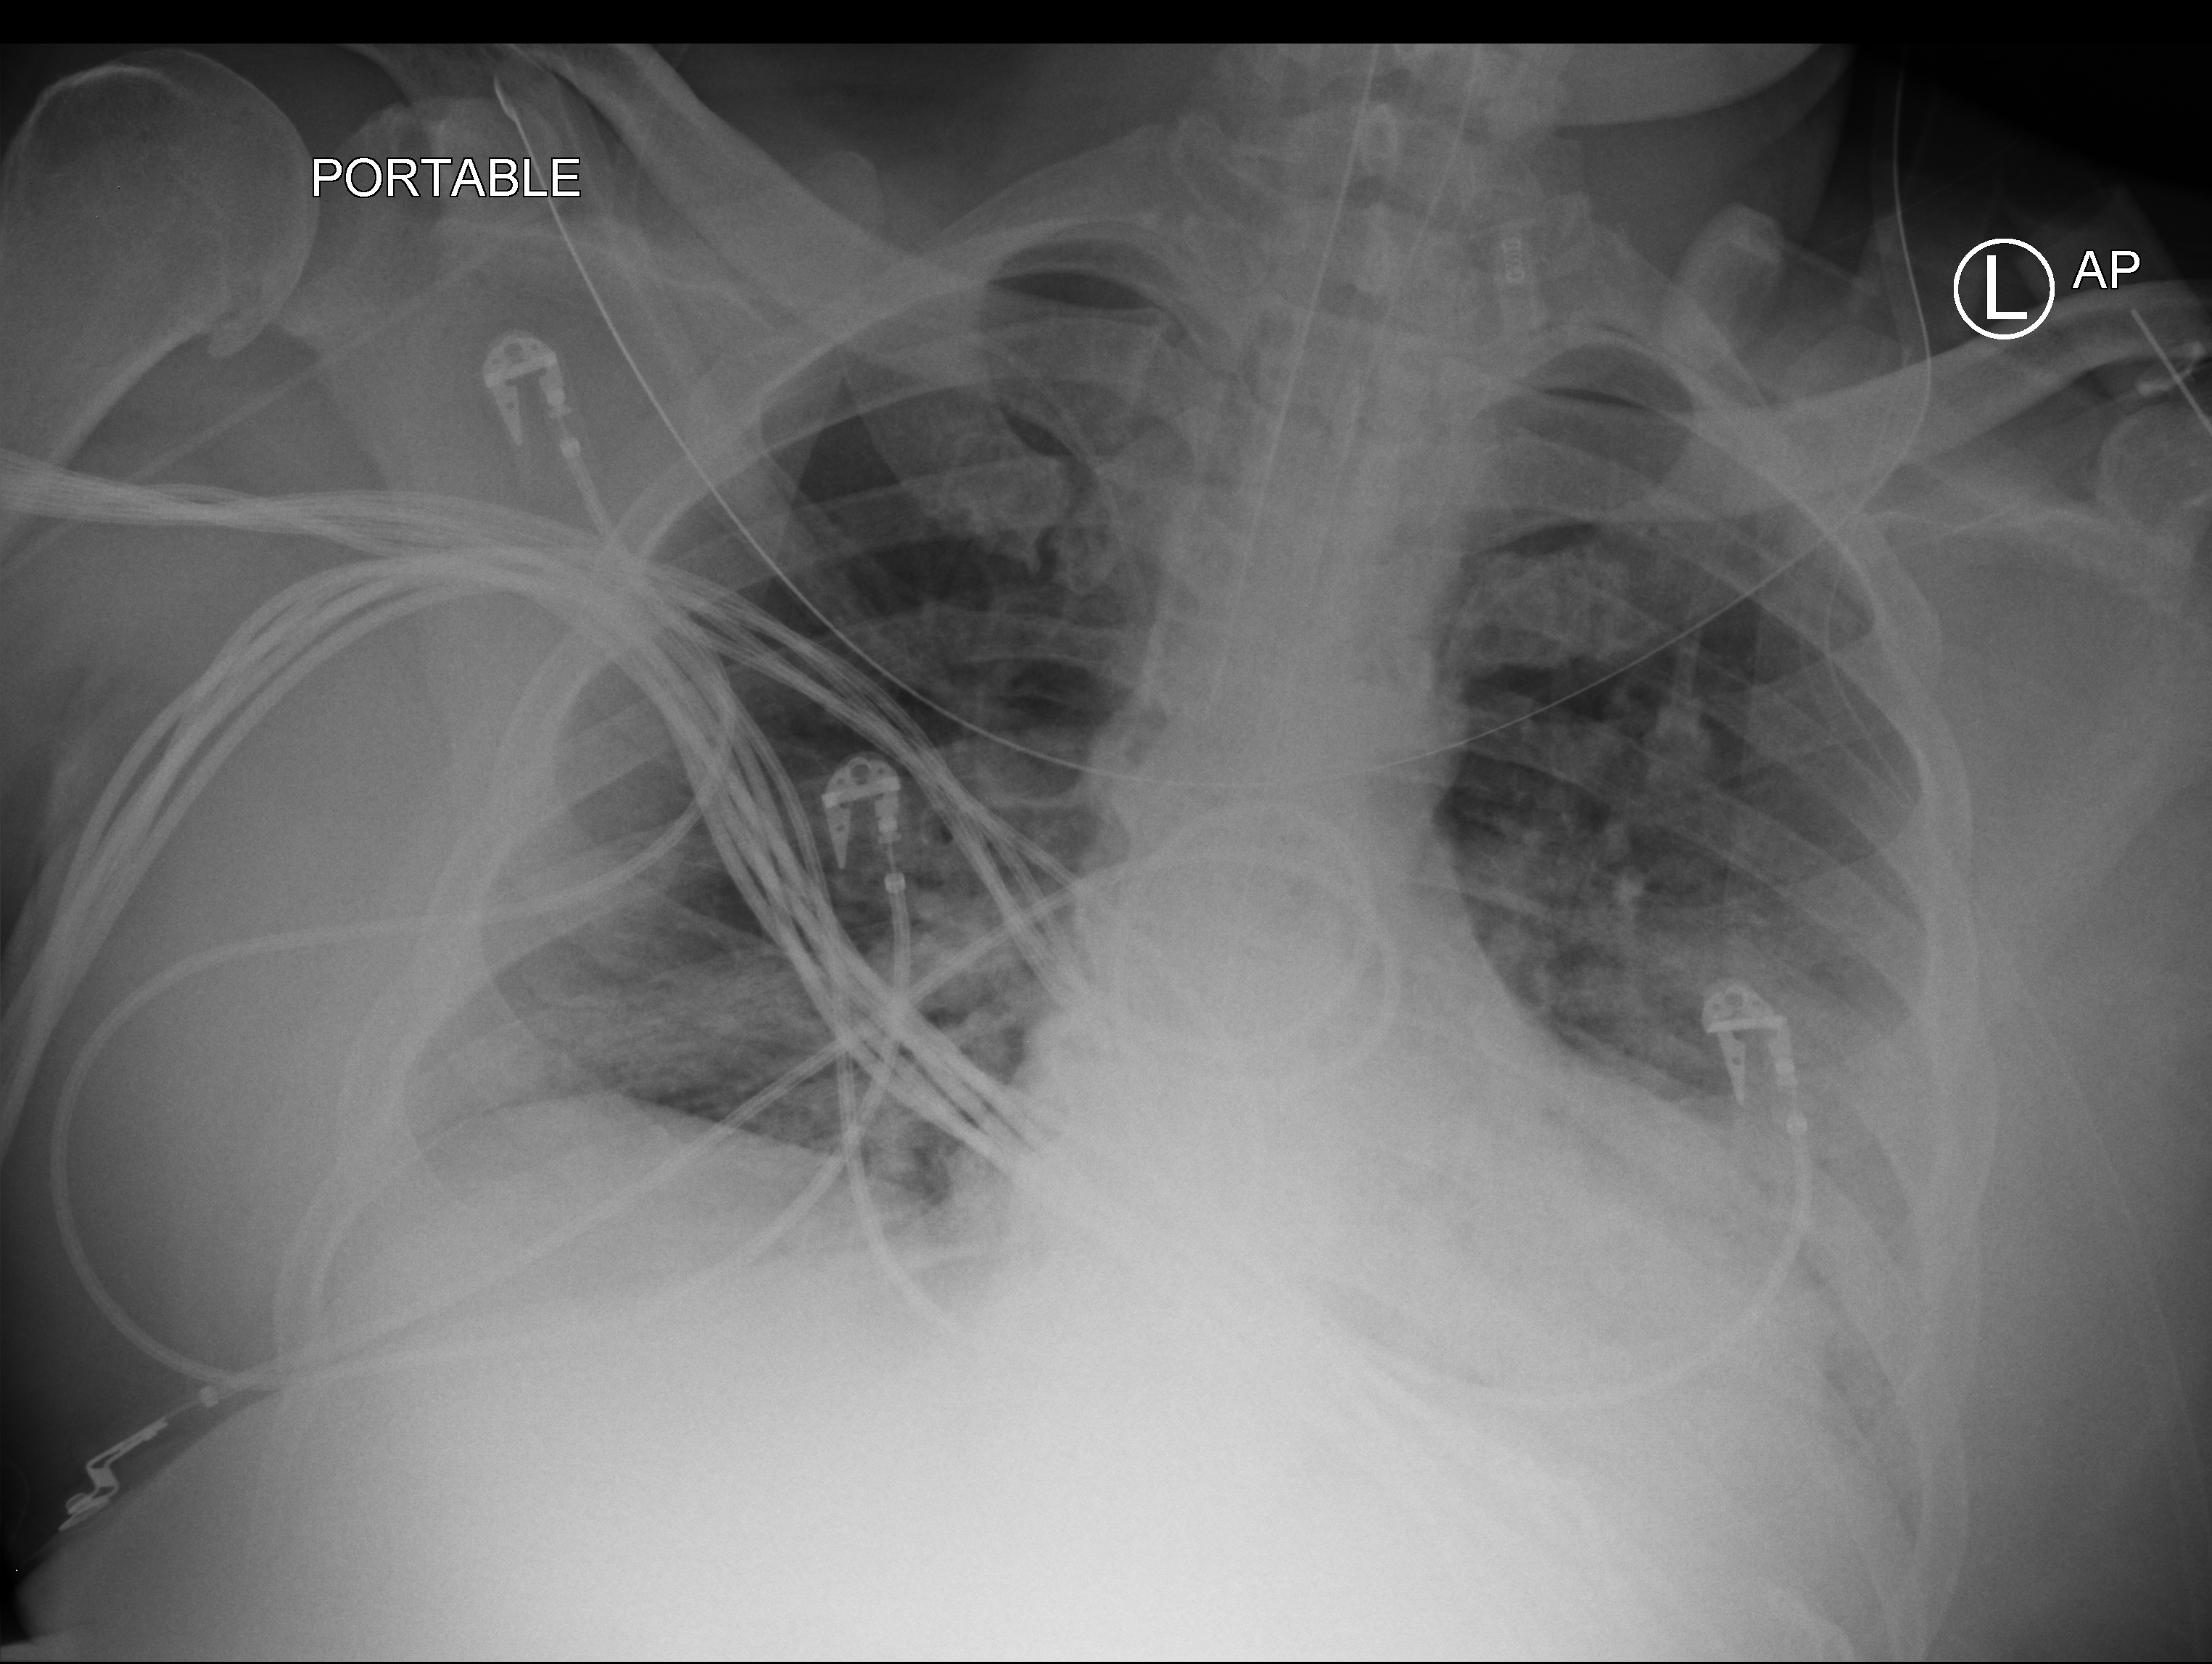
Chest X-ray (portable), anteroposterior (AP) projection. Male patient hospitalised with COVID-19, age 18–59 years.
From the hospital-stay record, not from the radiograph (when in the stay this image was taken is not recorded): diabetes (admission record): no; mechanically ventilated during this hospital stay: yes.